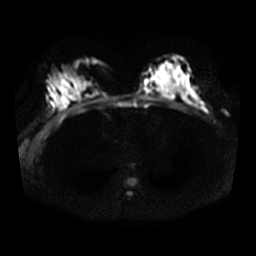
Breast MRI, one axial slice. Position 17 of 32 along the scan axis. Diffusion-weighted series; image 2 of 4 stored at this slice position (different b-values; order by instance number). 3 T. 5 mm slice thickness. 256 × 256 image matrix, field of view 340 × 340 mm. Female patient.
Structures marked on this image (manually delineated by an expert):
- tumour on diffusion-weighted imaging: bounding box <202,108,207,113> (left, top, right, bottom; pixels)